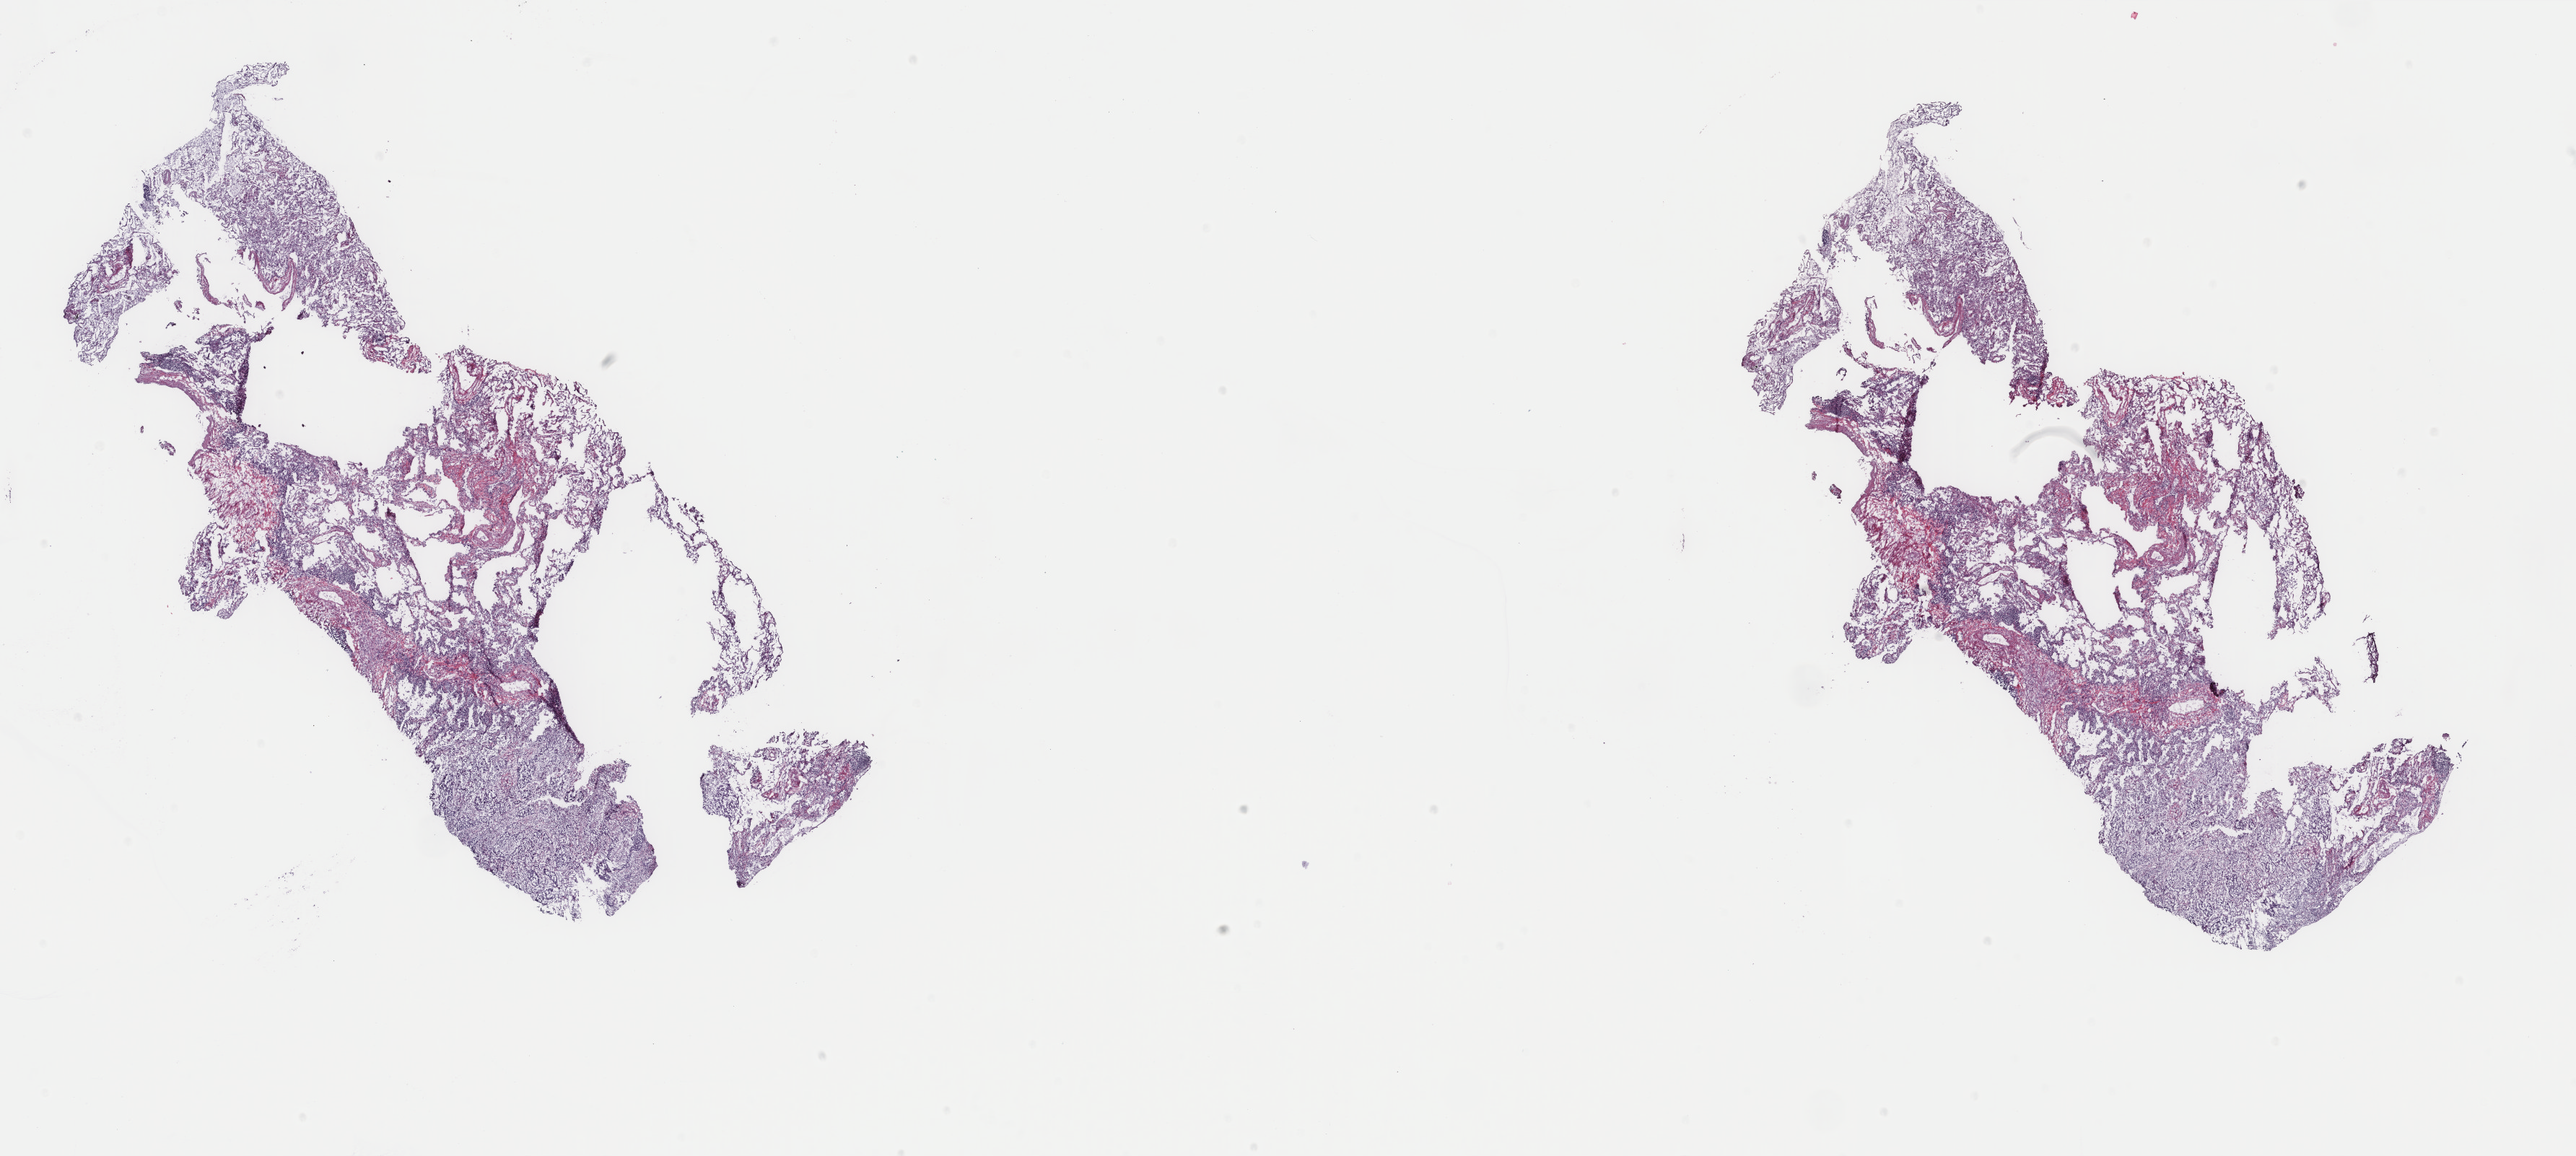
Digitized H&E tissue section (whole slide), shown as a low-resolution overview of the whole scanned area (about 28.3 x 12.7 mm, acquisition: 40x scan); frozen section; primary tumour sample from the lung. Patient: female, age at initial diagnosis 77 years. Slide review estimates, as recorded: tumour cells 50%, tumour nuclei 80%, normal cells 20%, stromal cells 30%, necrosis 0%. Inflammatory infiltration, as recorded: lymphocyte infiltration 10%, monocyte infiltration 6%, neutrophil infiltration 0%.
Diagnosis: Squamous cell carcinoma, NOS (lower lobe, lung). AJCC pathologic stage: IA (7th edition). TNM: T1a N0 M0.